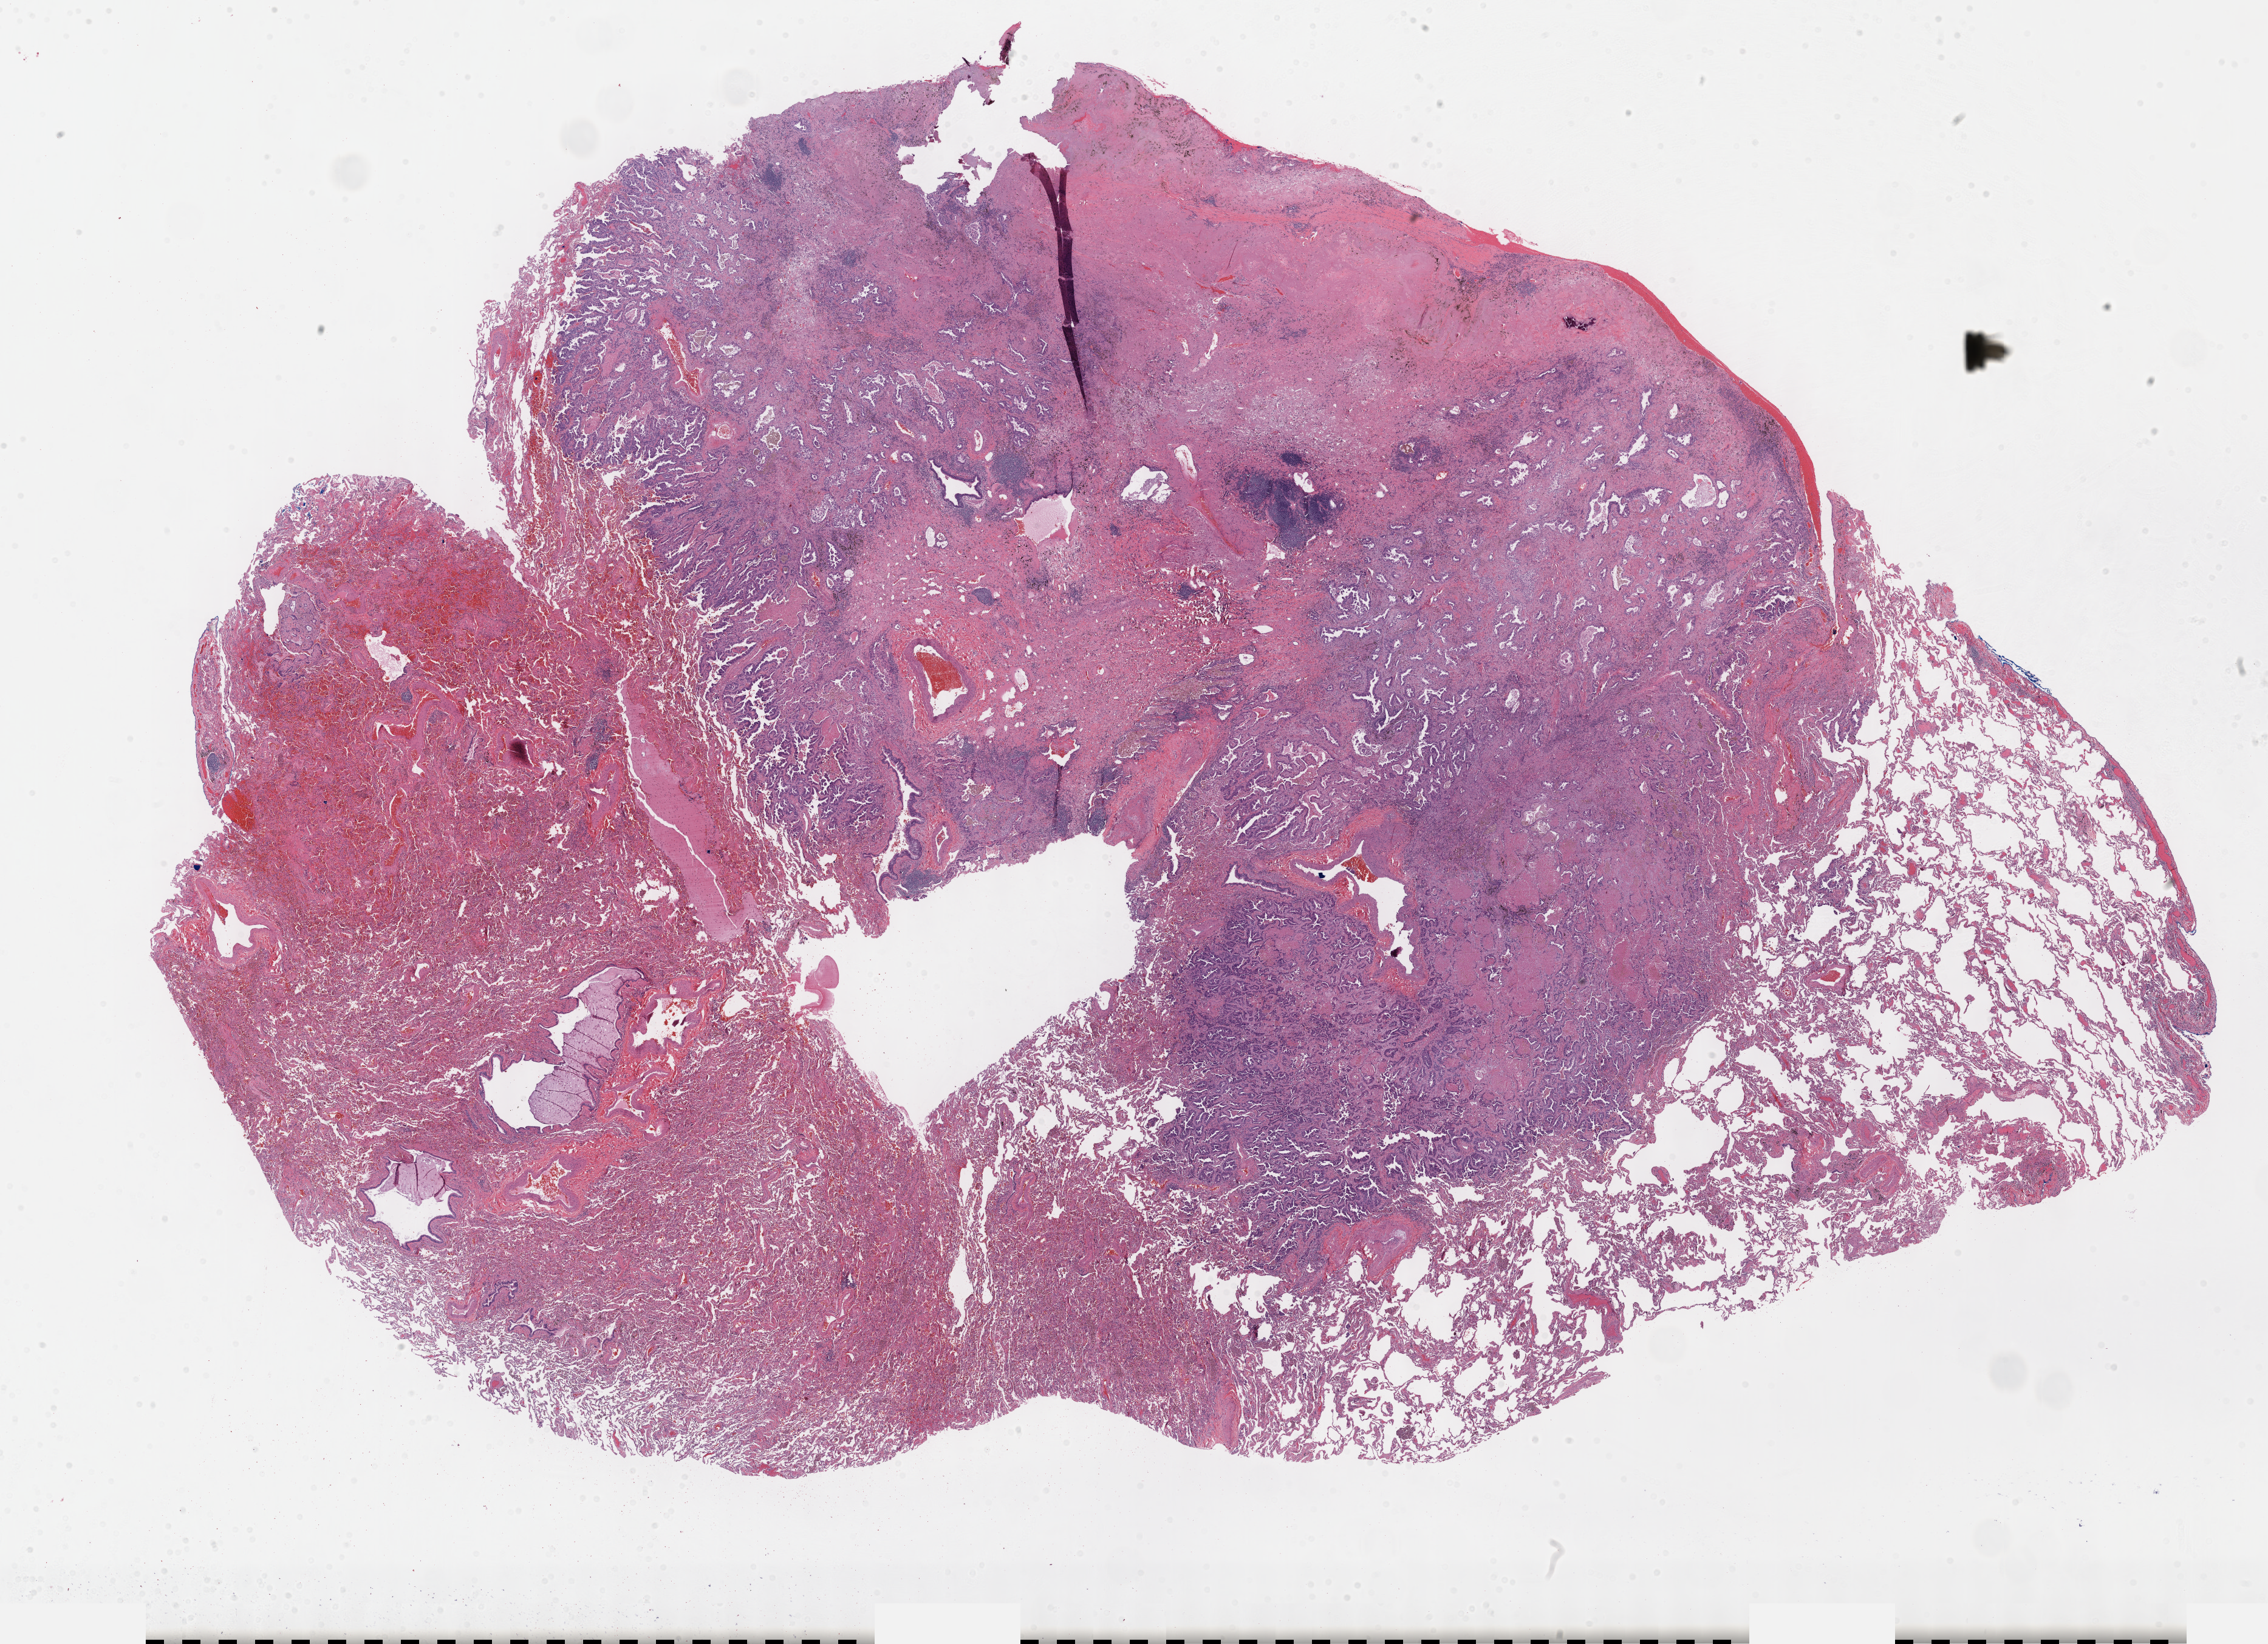
Whole-slide histology image, H&E-stained, a low-resolution overview of the entire scanned area, about 30.2 x 21.9 mm (acquisition: 40x scan), formalin-fixed paraffin-embedded (FFPE) diagnostic section, primary tumour sample from the lung. Male patient; age at initial diagnosis 57 years.
Pathologic diagnosis: Adenocarcinoma, NOS (upper lobe, lung). AJCC pathologic stage: IA (7th edition). TNM: T1b N0 M0.